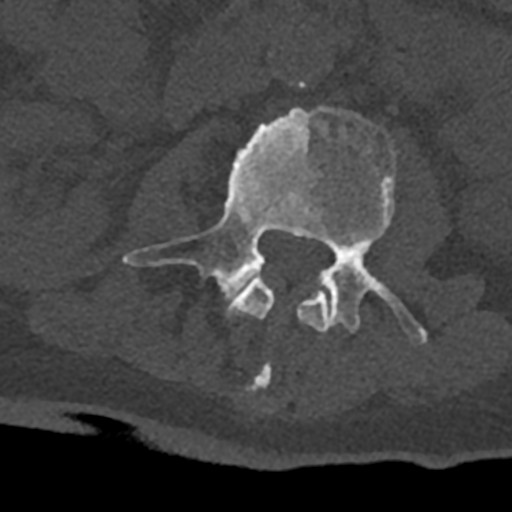
CT including the spine, one axial slice. 120 kVp. Bone window (W 1800 / L 400 HU). 0.5 mm slice thickness. 512 × 512 image matrix. Male patient, age 74 years. Case-level facts recorded for this patient, not image findings: primary cancer: renal; vertebrae with lytic lesions (as recorded): T10, L1, L2, L3, L4, L5.
Annotated regions visible in this slice (semi-automatically segmented with operator editing):
- L2 vertebra: bounding box (x1, y1, x2, y2) in pixels: (227, 276, 330, 391)
- L3 vertebra: (122, 106, 427, 344)